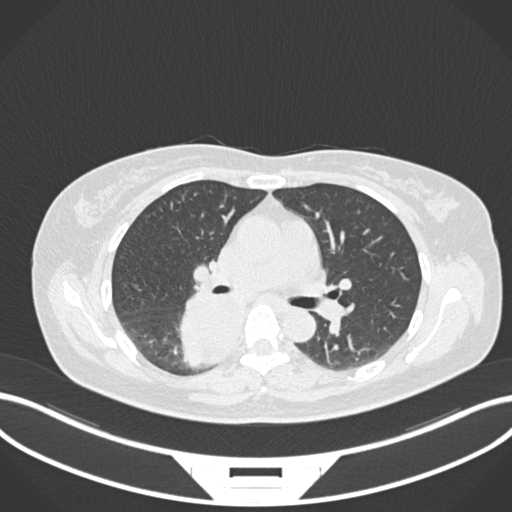
Chest CT, one axial slice; slice 607 of 677 in the series (ordered by position); reconstruction kernel B30f; lung window (W 1500 / L -600 HU); 1 mm slice thickness; 512 × 512 image matrix, field of view 400 × 400 mm. Female patient, age 54 years. Case-level facts recorded for this patient, not image findings: clinical TNM (as recorded): T4 N0 M0.
Structures marked on this image (rectangle marked by the reading radiologist):
- lung tumour (recorded histology: adenocarcinoma): bounding box (x1, y1, x2, y2) in pixels: (173, 288, 243, 370)